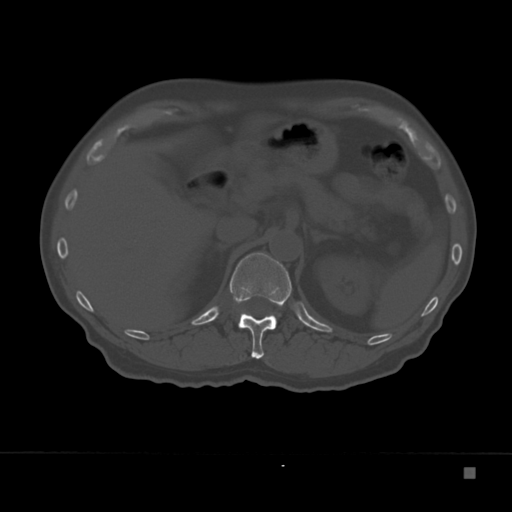
CT including the spine, one axial slice; position 128 of 332 along the scan axis; reconstruction kernel Br40s; 120 kVp; bone window (W 1800 / L 400 HU); 1.5 mm slice thickness; 512 × 512 image matrix. Male patient, age 72 years. From the clinical record (not read from this slice): primary cancer: skeletal.
Outlined on this slice (semi-automatically segmented with operator editing):
- T12 vertebra: bounding box <230,253,292,359> (left, top, right, bottom; pixels)